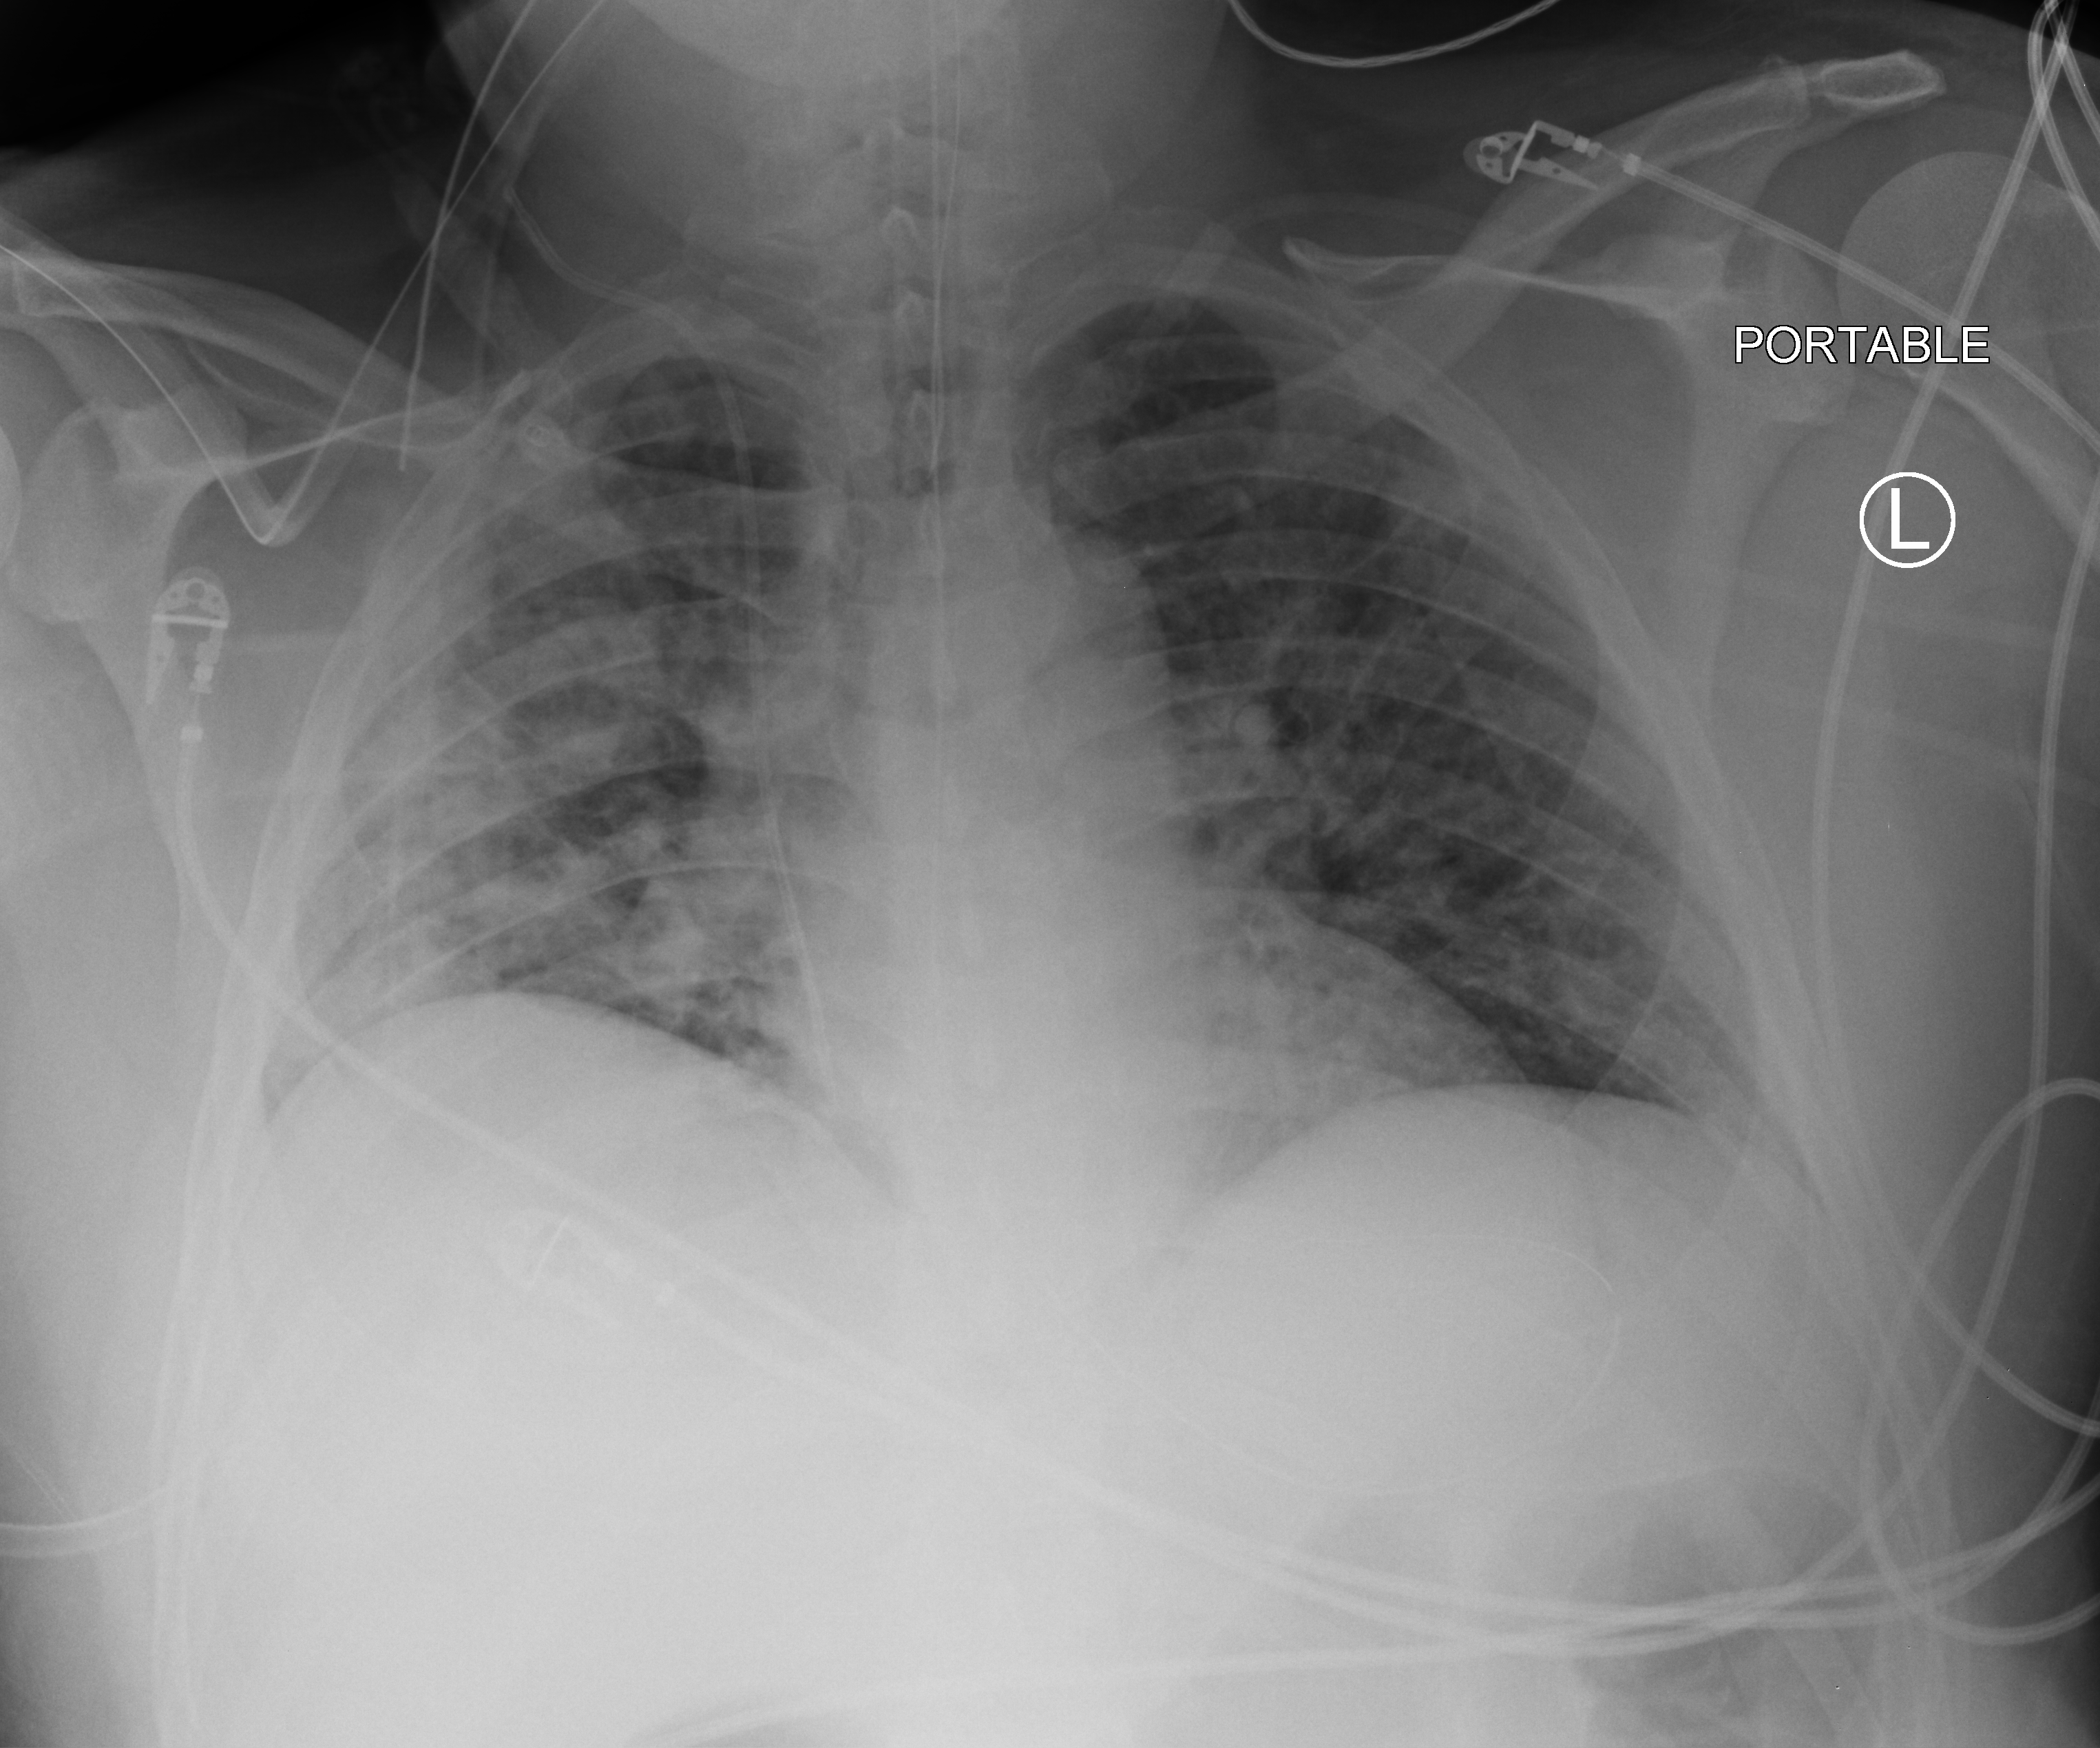
Bedside chest radiograph (computed radiography). Patient hospitalised with COVID-19; male, aged 18–59 years.
Hospital-stay facts (about this admission, not read from this image; timing relative to this image not recorded):
- admitted to intensive care during this hospital stay: yes
- length of hospital stay: 22 days